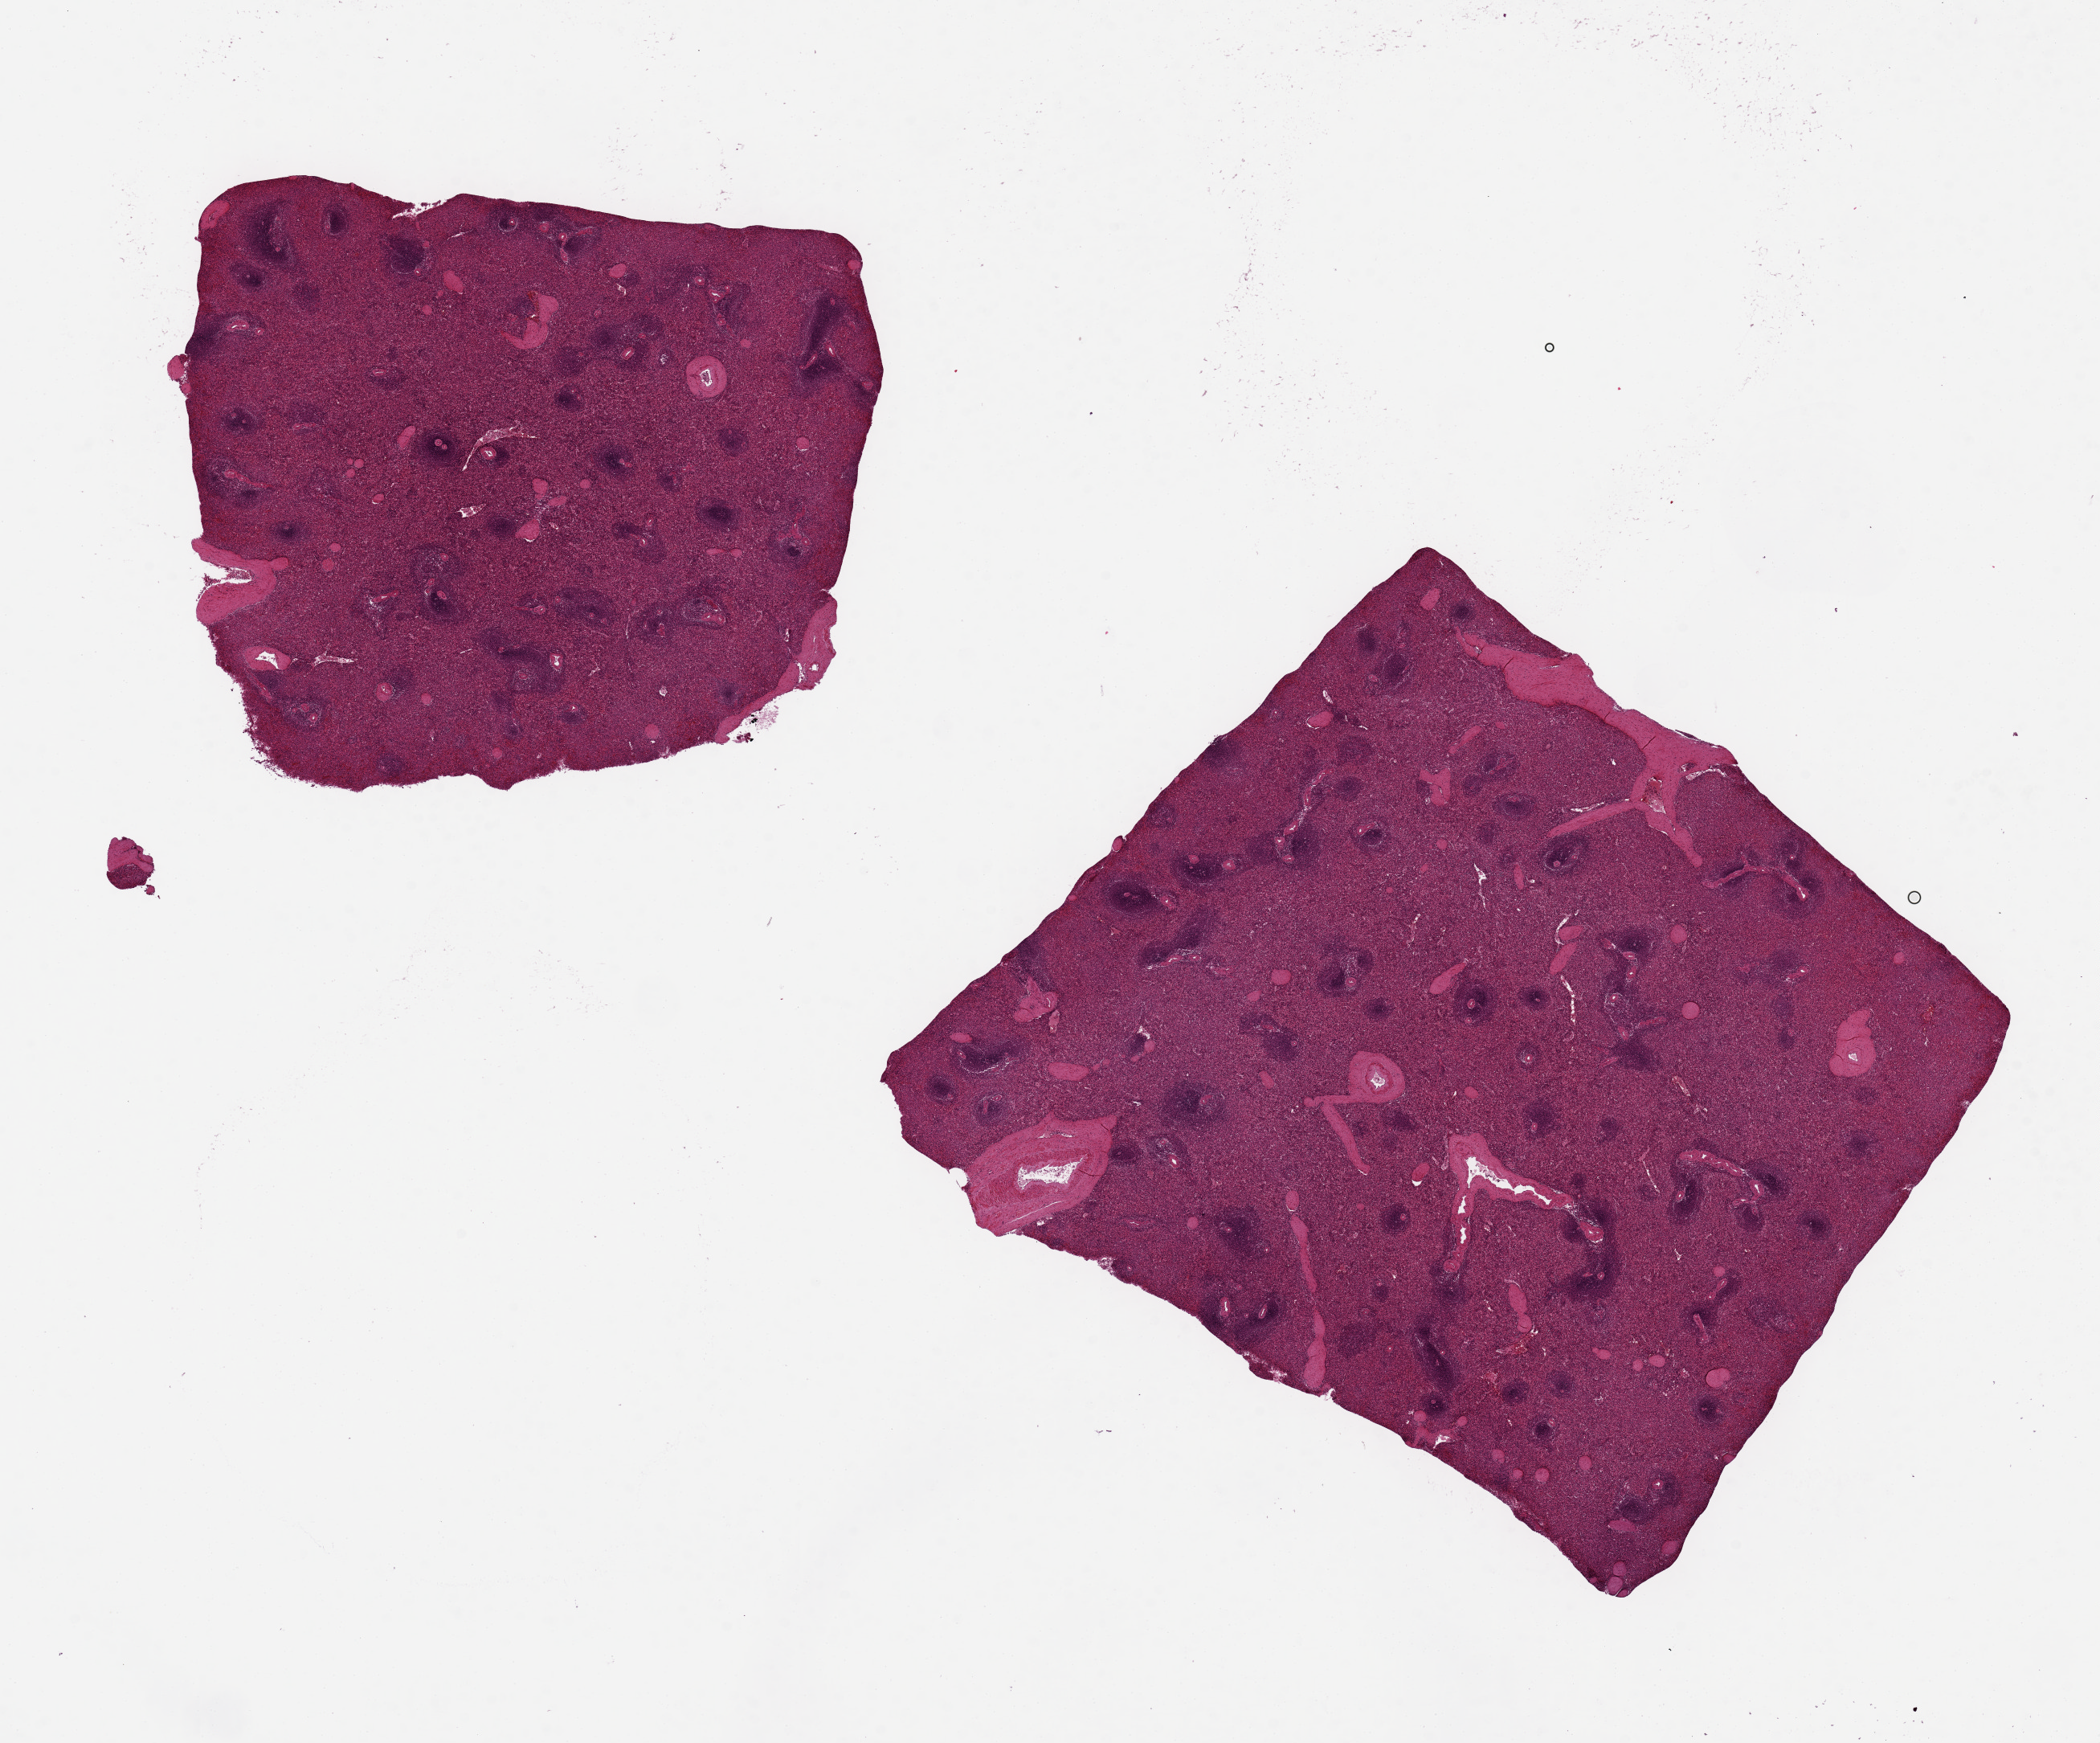
Digitized hematoxylin and eosin (H&E)-stained section, brightfield — shown as a low-resolution overview of the whole scanned area (about 20.7 x 17.2 mm, slide scanned at 20x); PAXgene-fixed, paraffin-embedded tissue; target tissue: spleen; donor tissue sample. Donor sex: male.
Review note (as recorded): 2 pieces, 6x7 & 8x9 mm; not congested.